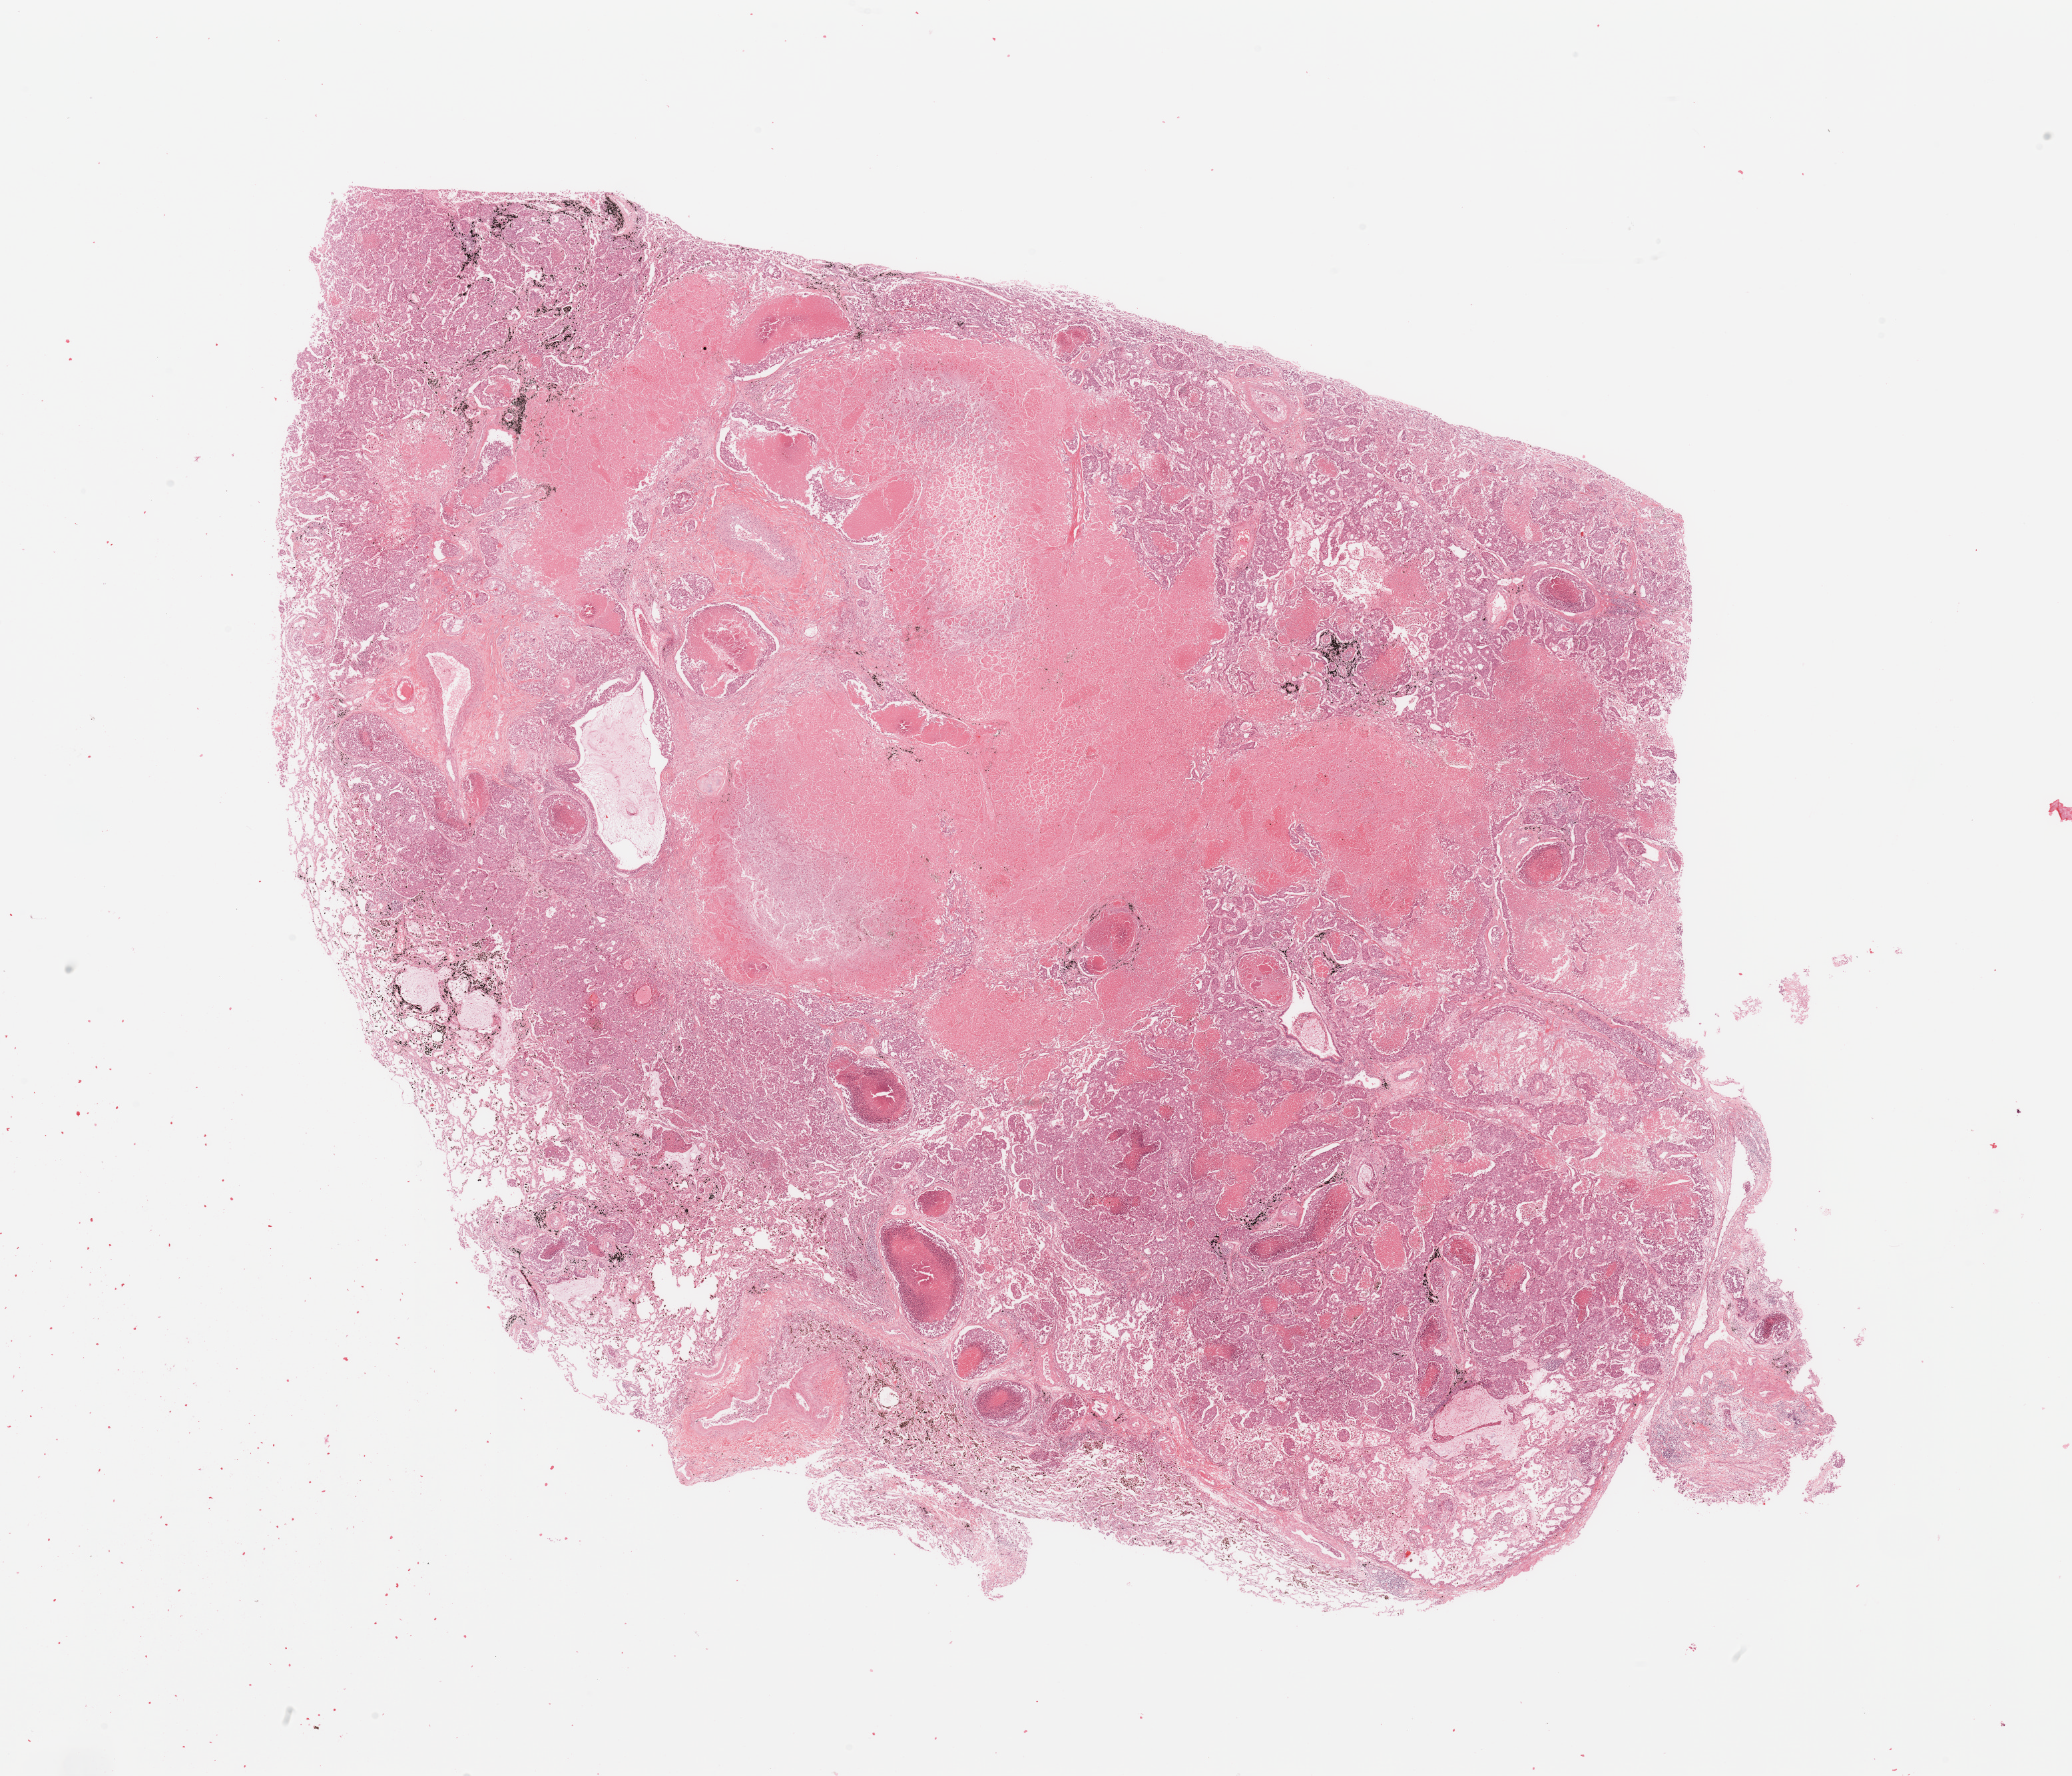
Hematoxylin and eosin (H&E) stained whole-slide image, whole scanned area (about 24.6 x 21.1 mm, slide scanned at 20x) shown as a low-resolution overview; lung, tumour tissue. 56-year-old male patient. Histologic grade: G3 (poorly differentiated).
AJCC pathologic stage: IIIA. Diagnosis: Adenocarcinoma, NOS.